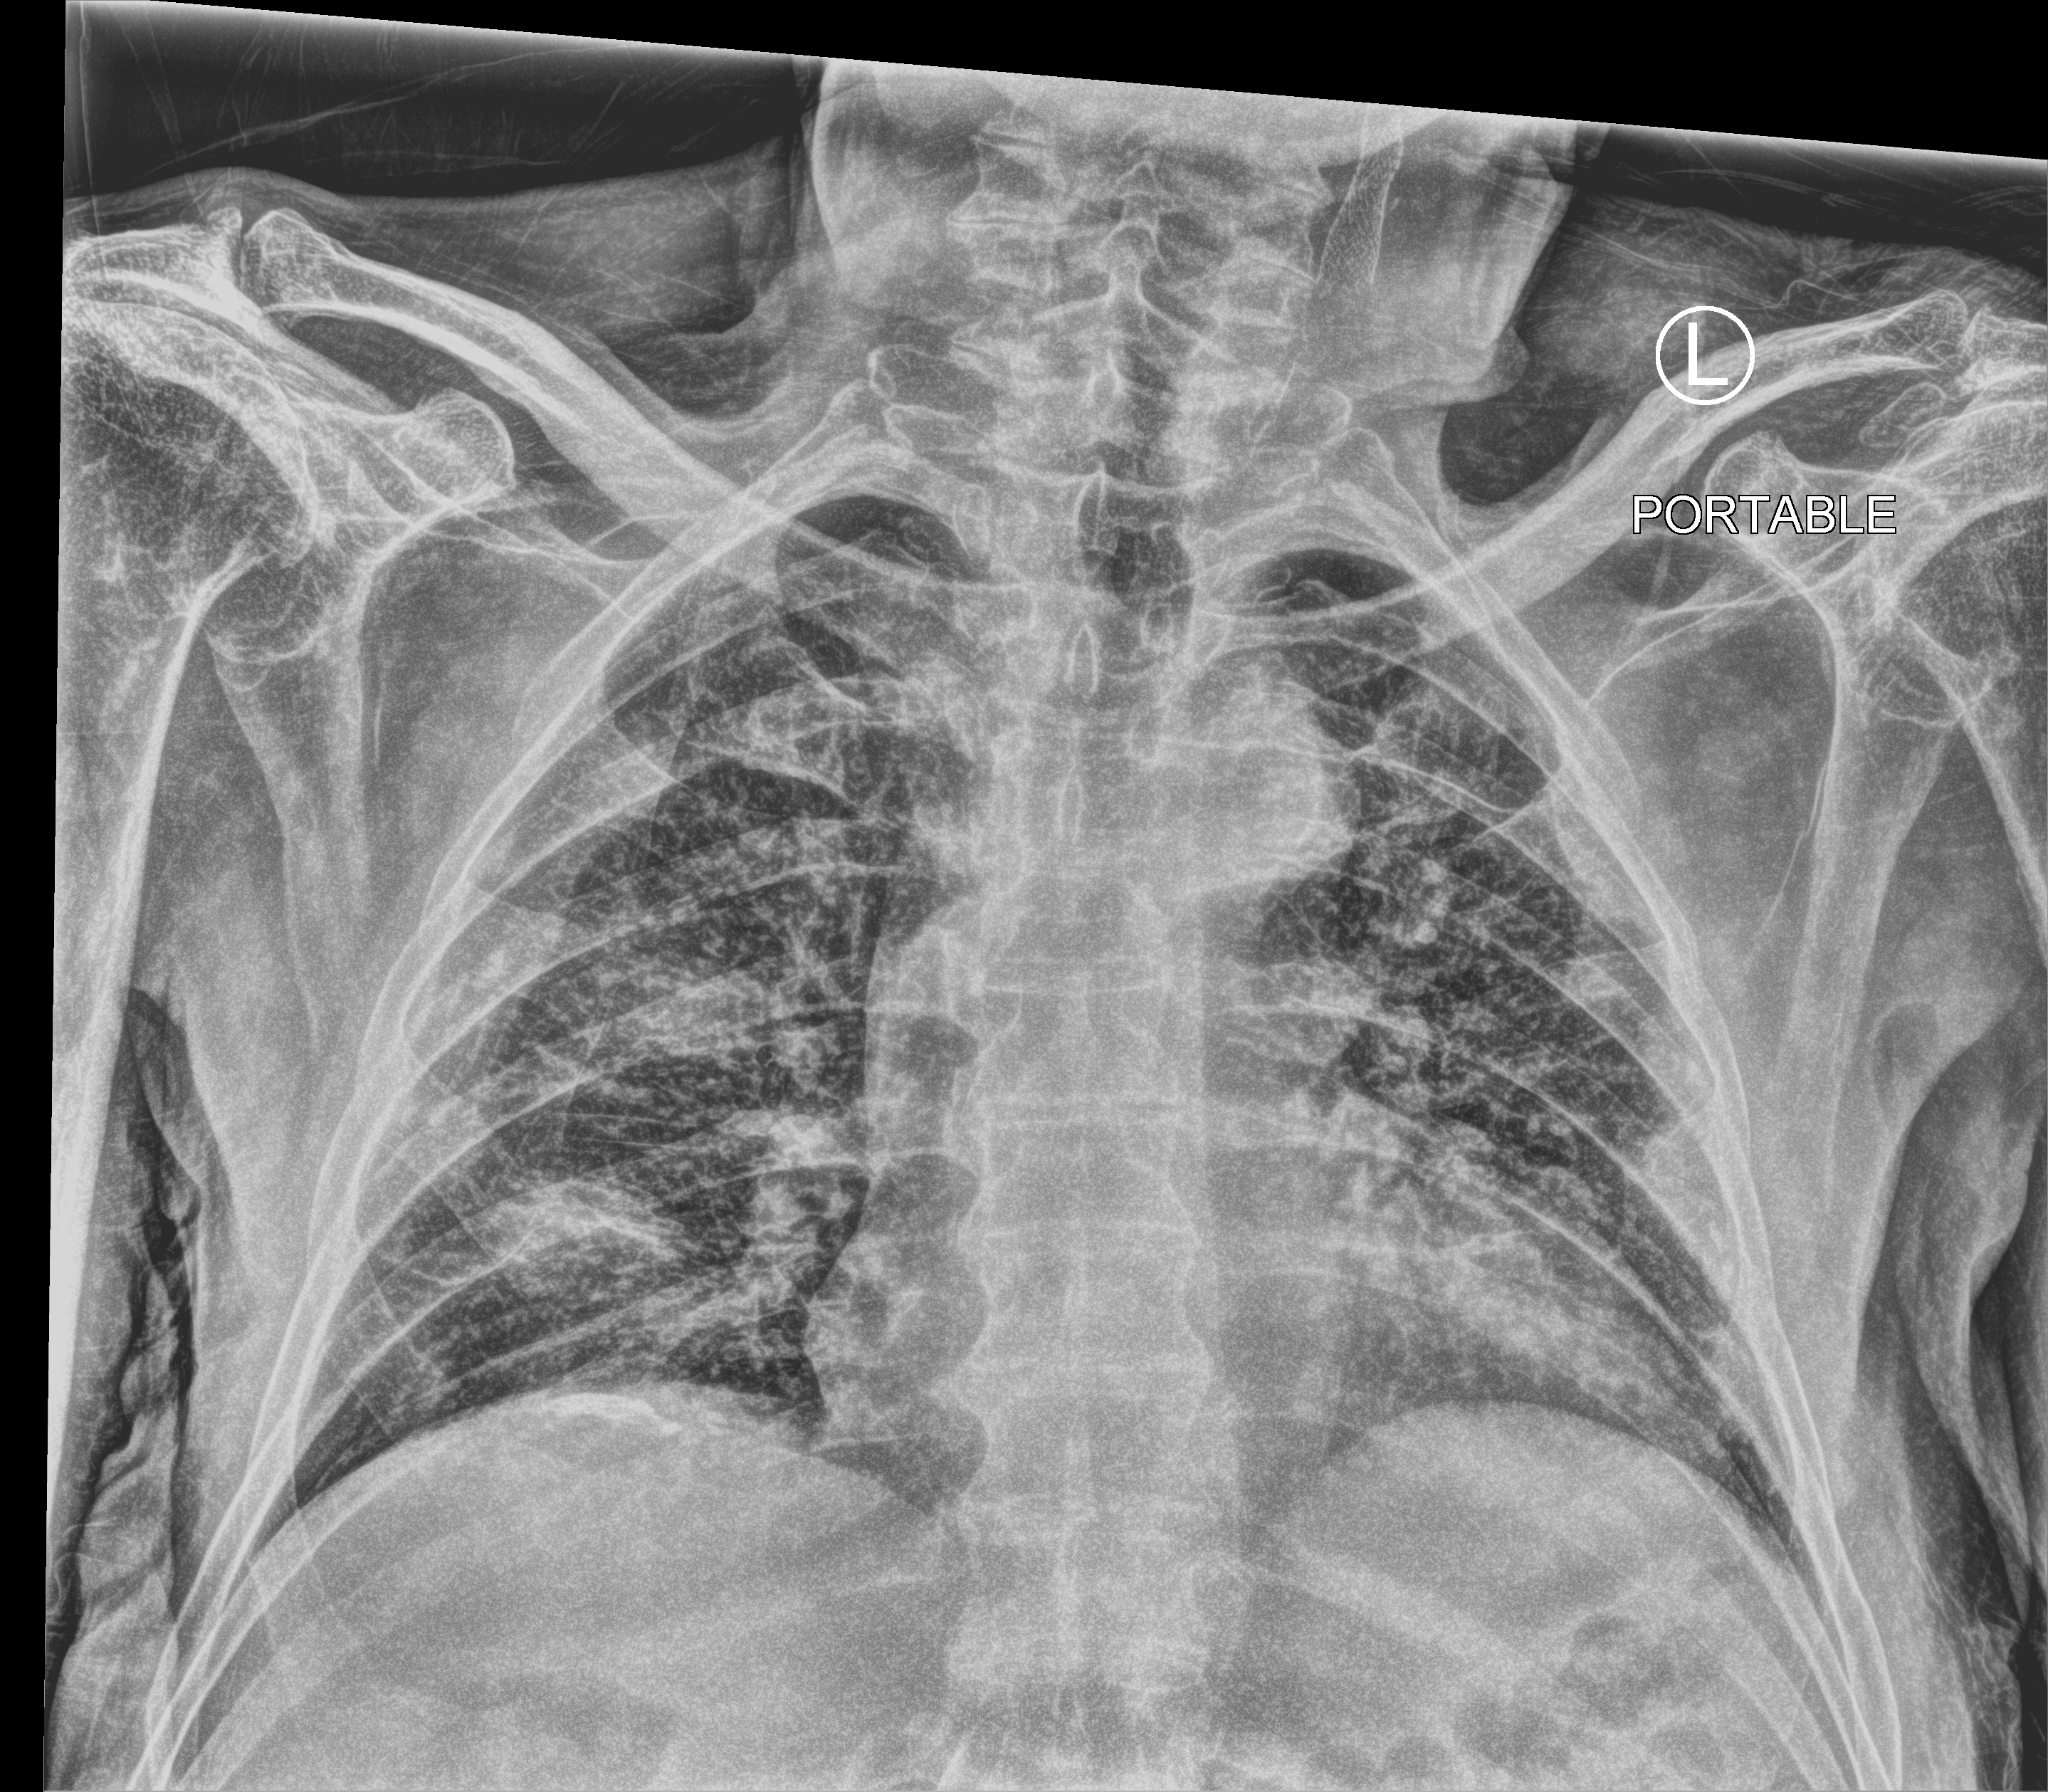
Bedside chest radiograph (computed radiography), anteroposterior (AP) projection. Patient hospitalised with COVID-19; male, aged 75–90 years.
Hospital-stay facts (about this admission, not read from this image; timing relative to this image not recorded): admitted to intensive care during this hospital stay: no; mechanically ventilated during this hospital stay: no.